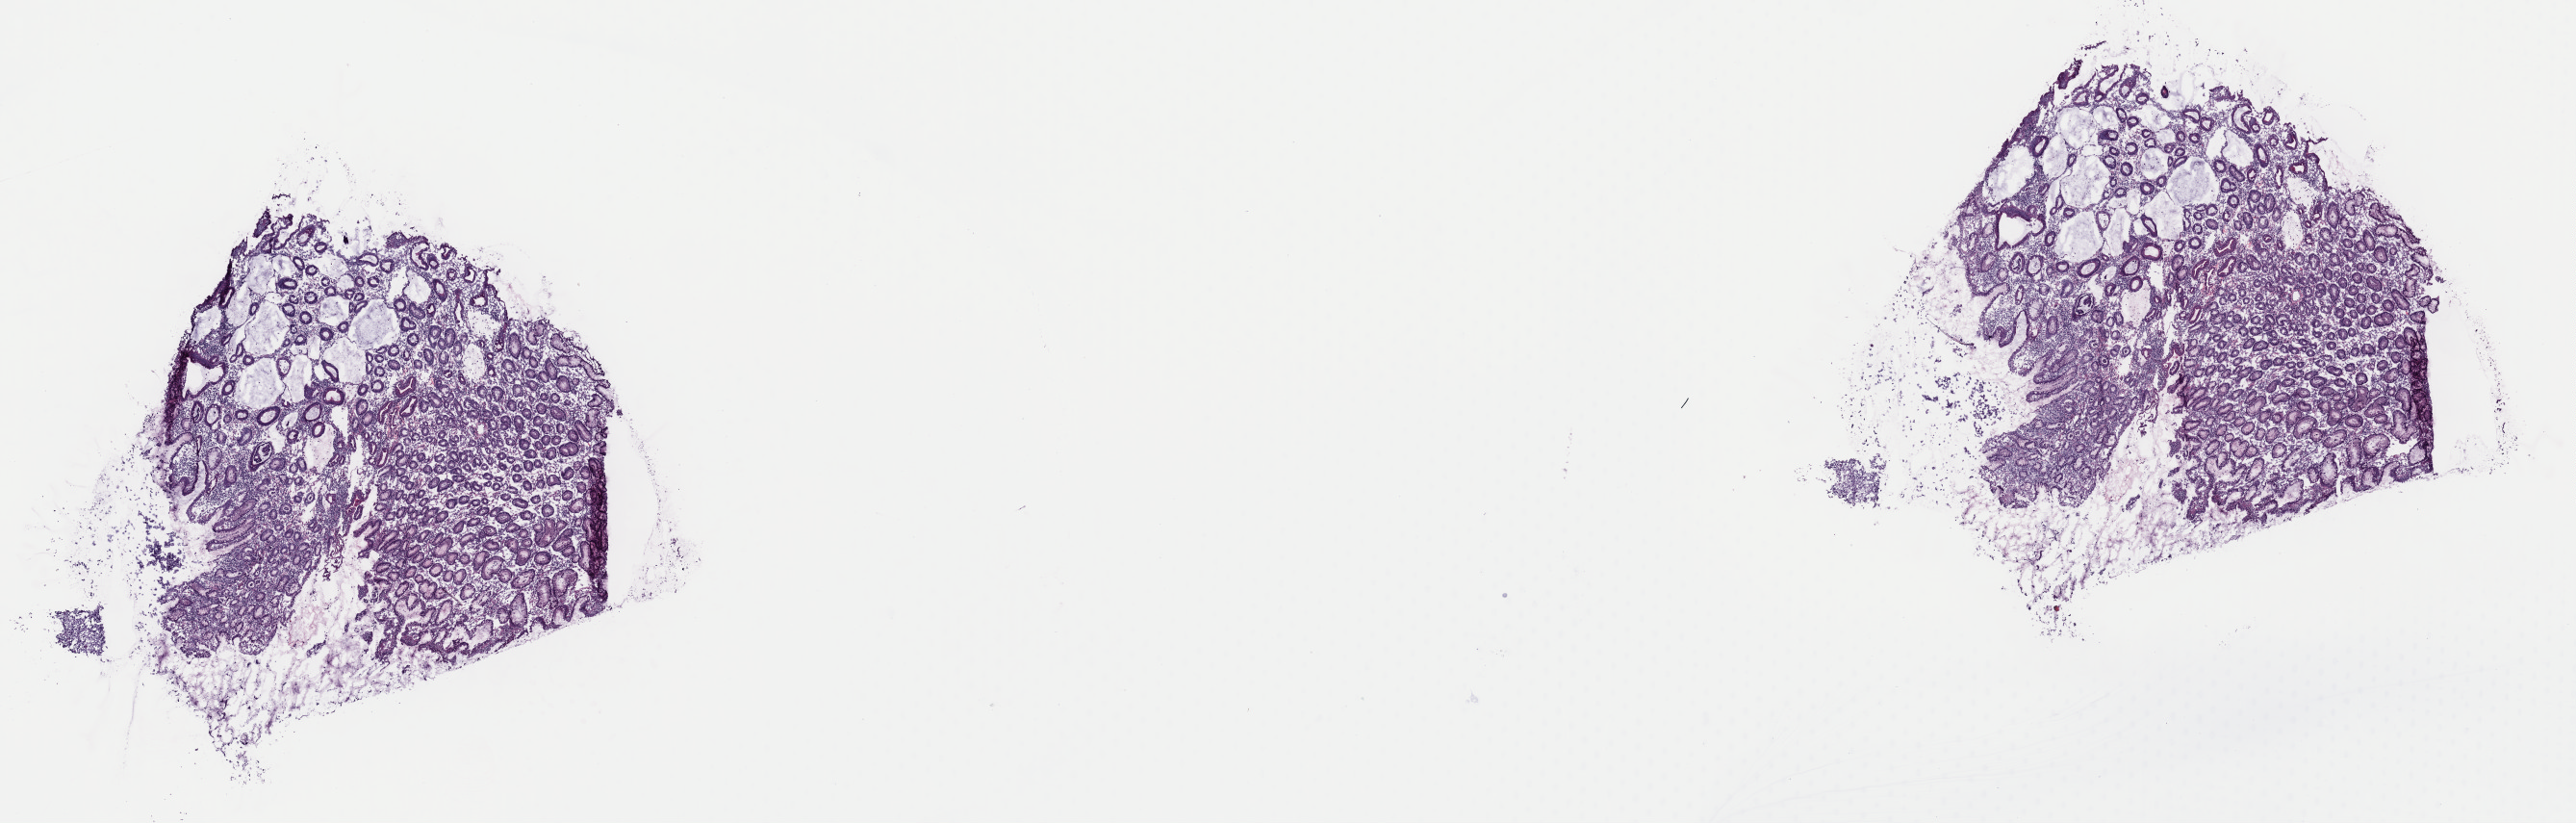
Whole-slide histology image, Hematoxylin and eosin (H&E) stained — low-resolution overview of the scanned area, about 21.1 x 6.8 mm (acquisition: 40x scan), frozen section from the top of the tissue portion, sample: primary tumour, stomach. Male, age 68 years at initial diagnosis. Histologic grade: G3 (poorly differentiated). Composition of this section per pathologist review: tumour cells 5%, tumour nuclei 5%, normal cells 95%, stromal cells 0%, necrosis 0%. Infiltration values recorded for this section: lymphocyte infiltration 15%, monocyte infiltration 2%, neutrophil infiltration 1%.
- pathologic diagnosis: Carcinoma, diffuse type (gastric antrum)
- AJCC pathologic stage: IIB (7th edition)
- TNM: T2 N2 M0